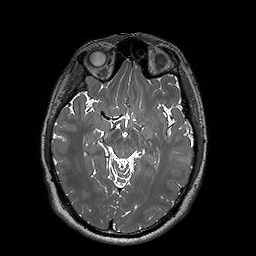
Brain MRI from a brain-tumour surgery series, one axial slice; position 99 of 192 along the scan axis; 1 mm slice thickness; 256 × 256 image matrix, field of view 250 × 250 mm. From the clinical record (not read from this slice): histopathology: Oligodendroglioma; WHO grade: 2; IDH mutation: yes.
Outlined on this slice (expert manual segmentation):
- tumour: bounding box [x1, y1, x2, y2] px = [171, 156, 185, 164]